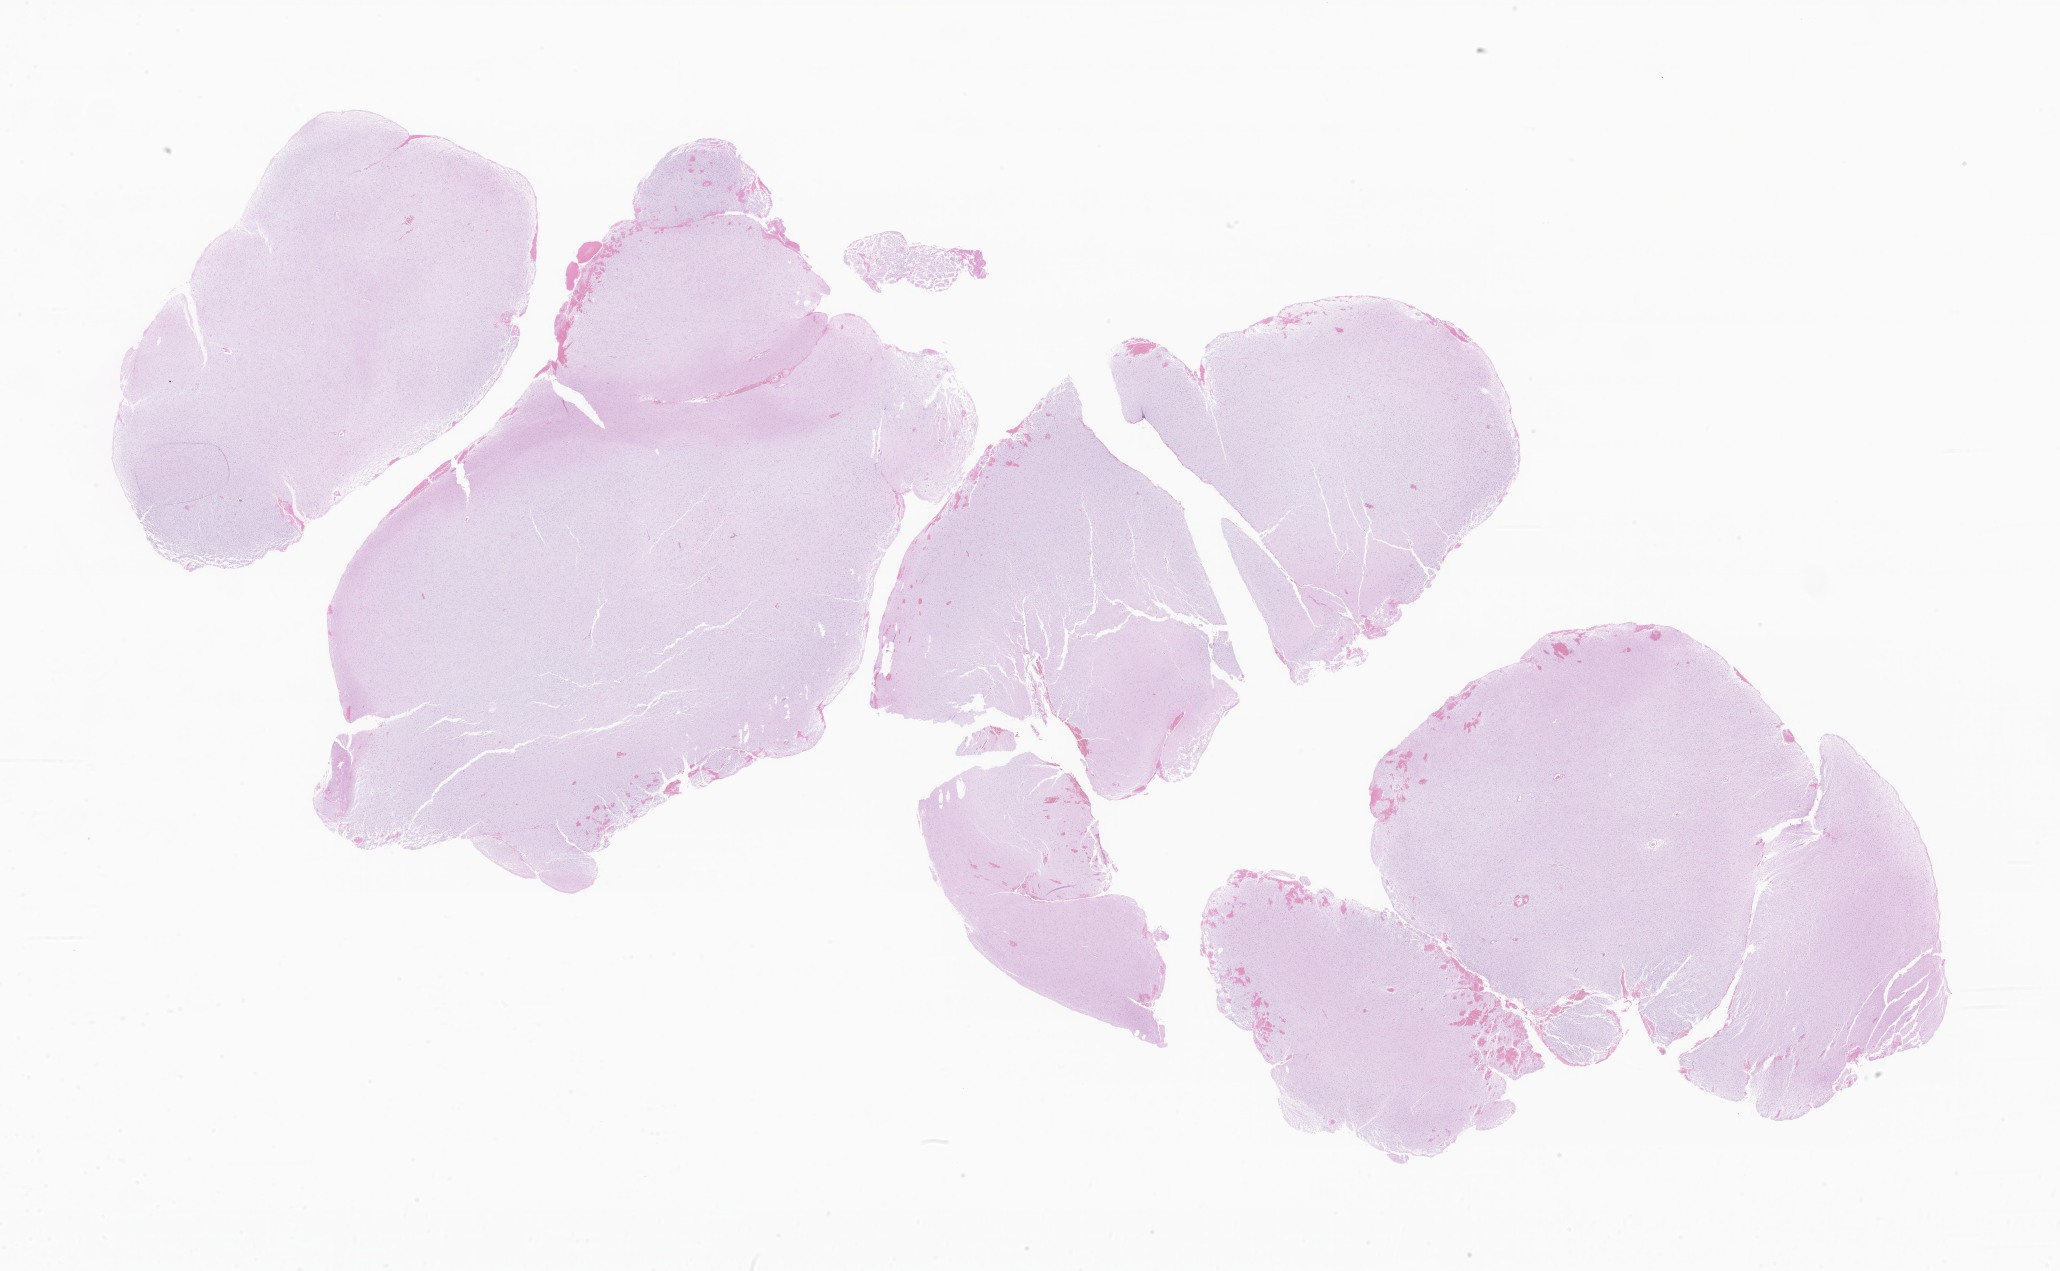
Haematoxylin and eosin whole-slide image of tumor tissue from the temporal lobe, whole scanned area (about 34.8 x 21.4 mm) shown as a low-resolution overview, formalin-fixed, paraffin-embedded (FFPE) tissue. Patient male; age 41 months (3 years 5 months).
Diagnosis: Ganglioglioma, NOS.